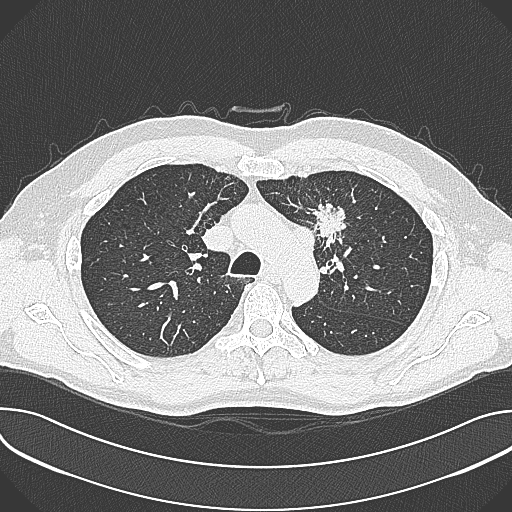
Low-dose screening chest CT, axial slice, baseline screening round, lung window (W 1500 / L -600 HU), lung (sharp) reconstruction kernel (B80f), 120 kVp, slice 96 of 361 in the series. Male, age 59 years at enrolment. Current smoker at enrolment.
Expert-annotated lung lesion, bounding box (x1, y1, x2, y2) in pixels: (302, 199, 360, 258). The screening reader recorded 2 non-calcified nodules or masses ≥4 mm on this exam (left upper lobe, left upper lobe); which of them this box marks is not recorded. Later outcome: lung cancer diagnosed 21 days after this screen — non-small cell carcinoma, left upper lobe, poorly differentiated (G3), stage IIIA (AJCC 6th edition), 35 mm at pathology.